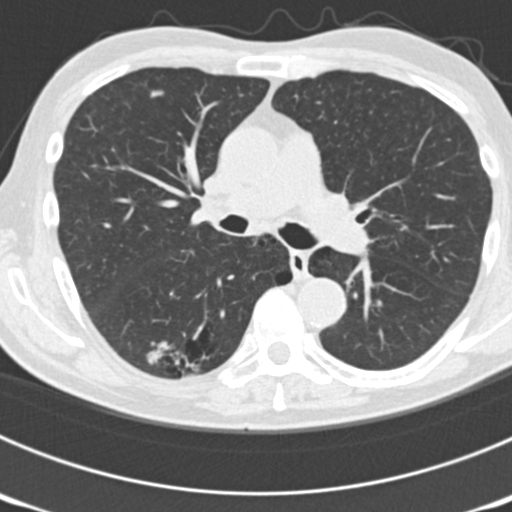
Low-dose screening chest CT, one axial slice; slice 112 of 177 in the series (ordered by position); reconstruction kernel B30f; lung window (W 1500 / L -600 HU); 2 mm slice thickness; 512 × 512 image matrix, field of view 300 × 300 mm.
Structures marked on this image (manually delineated by an expert):
- lesion 1 (nodule, upper lobe of right lung): box from (x=150, y=90) to (x=165, y=98) px